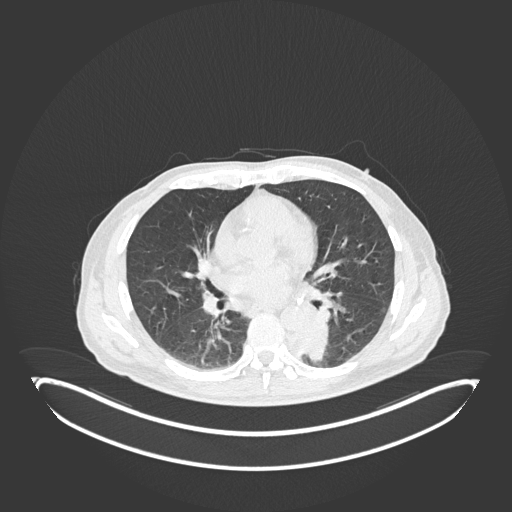
Chest CT, one axial slice; position 95 of 251 along the scan axis; reconstruction kernel B30f; lung window (W 1500 / L -600 HU); 512 × 512 image matrix, field of view 500 × 500 mm. Male patient, age 72 years. Case-level facts recorded for this patient, not image findings: clinical TNM (as recorded): T2b N0 M1.
Structures marked on this image (rectangle marked by the reading radiologist):
- lung tumour (recorded histology: adenocarcinoma): bounding box <285,314,330,366> (left, top, right, bottom; pixels)